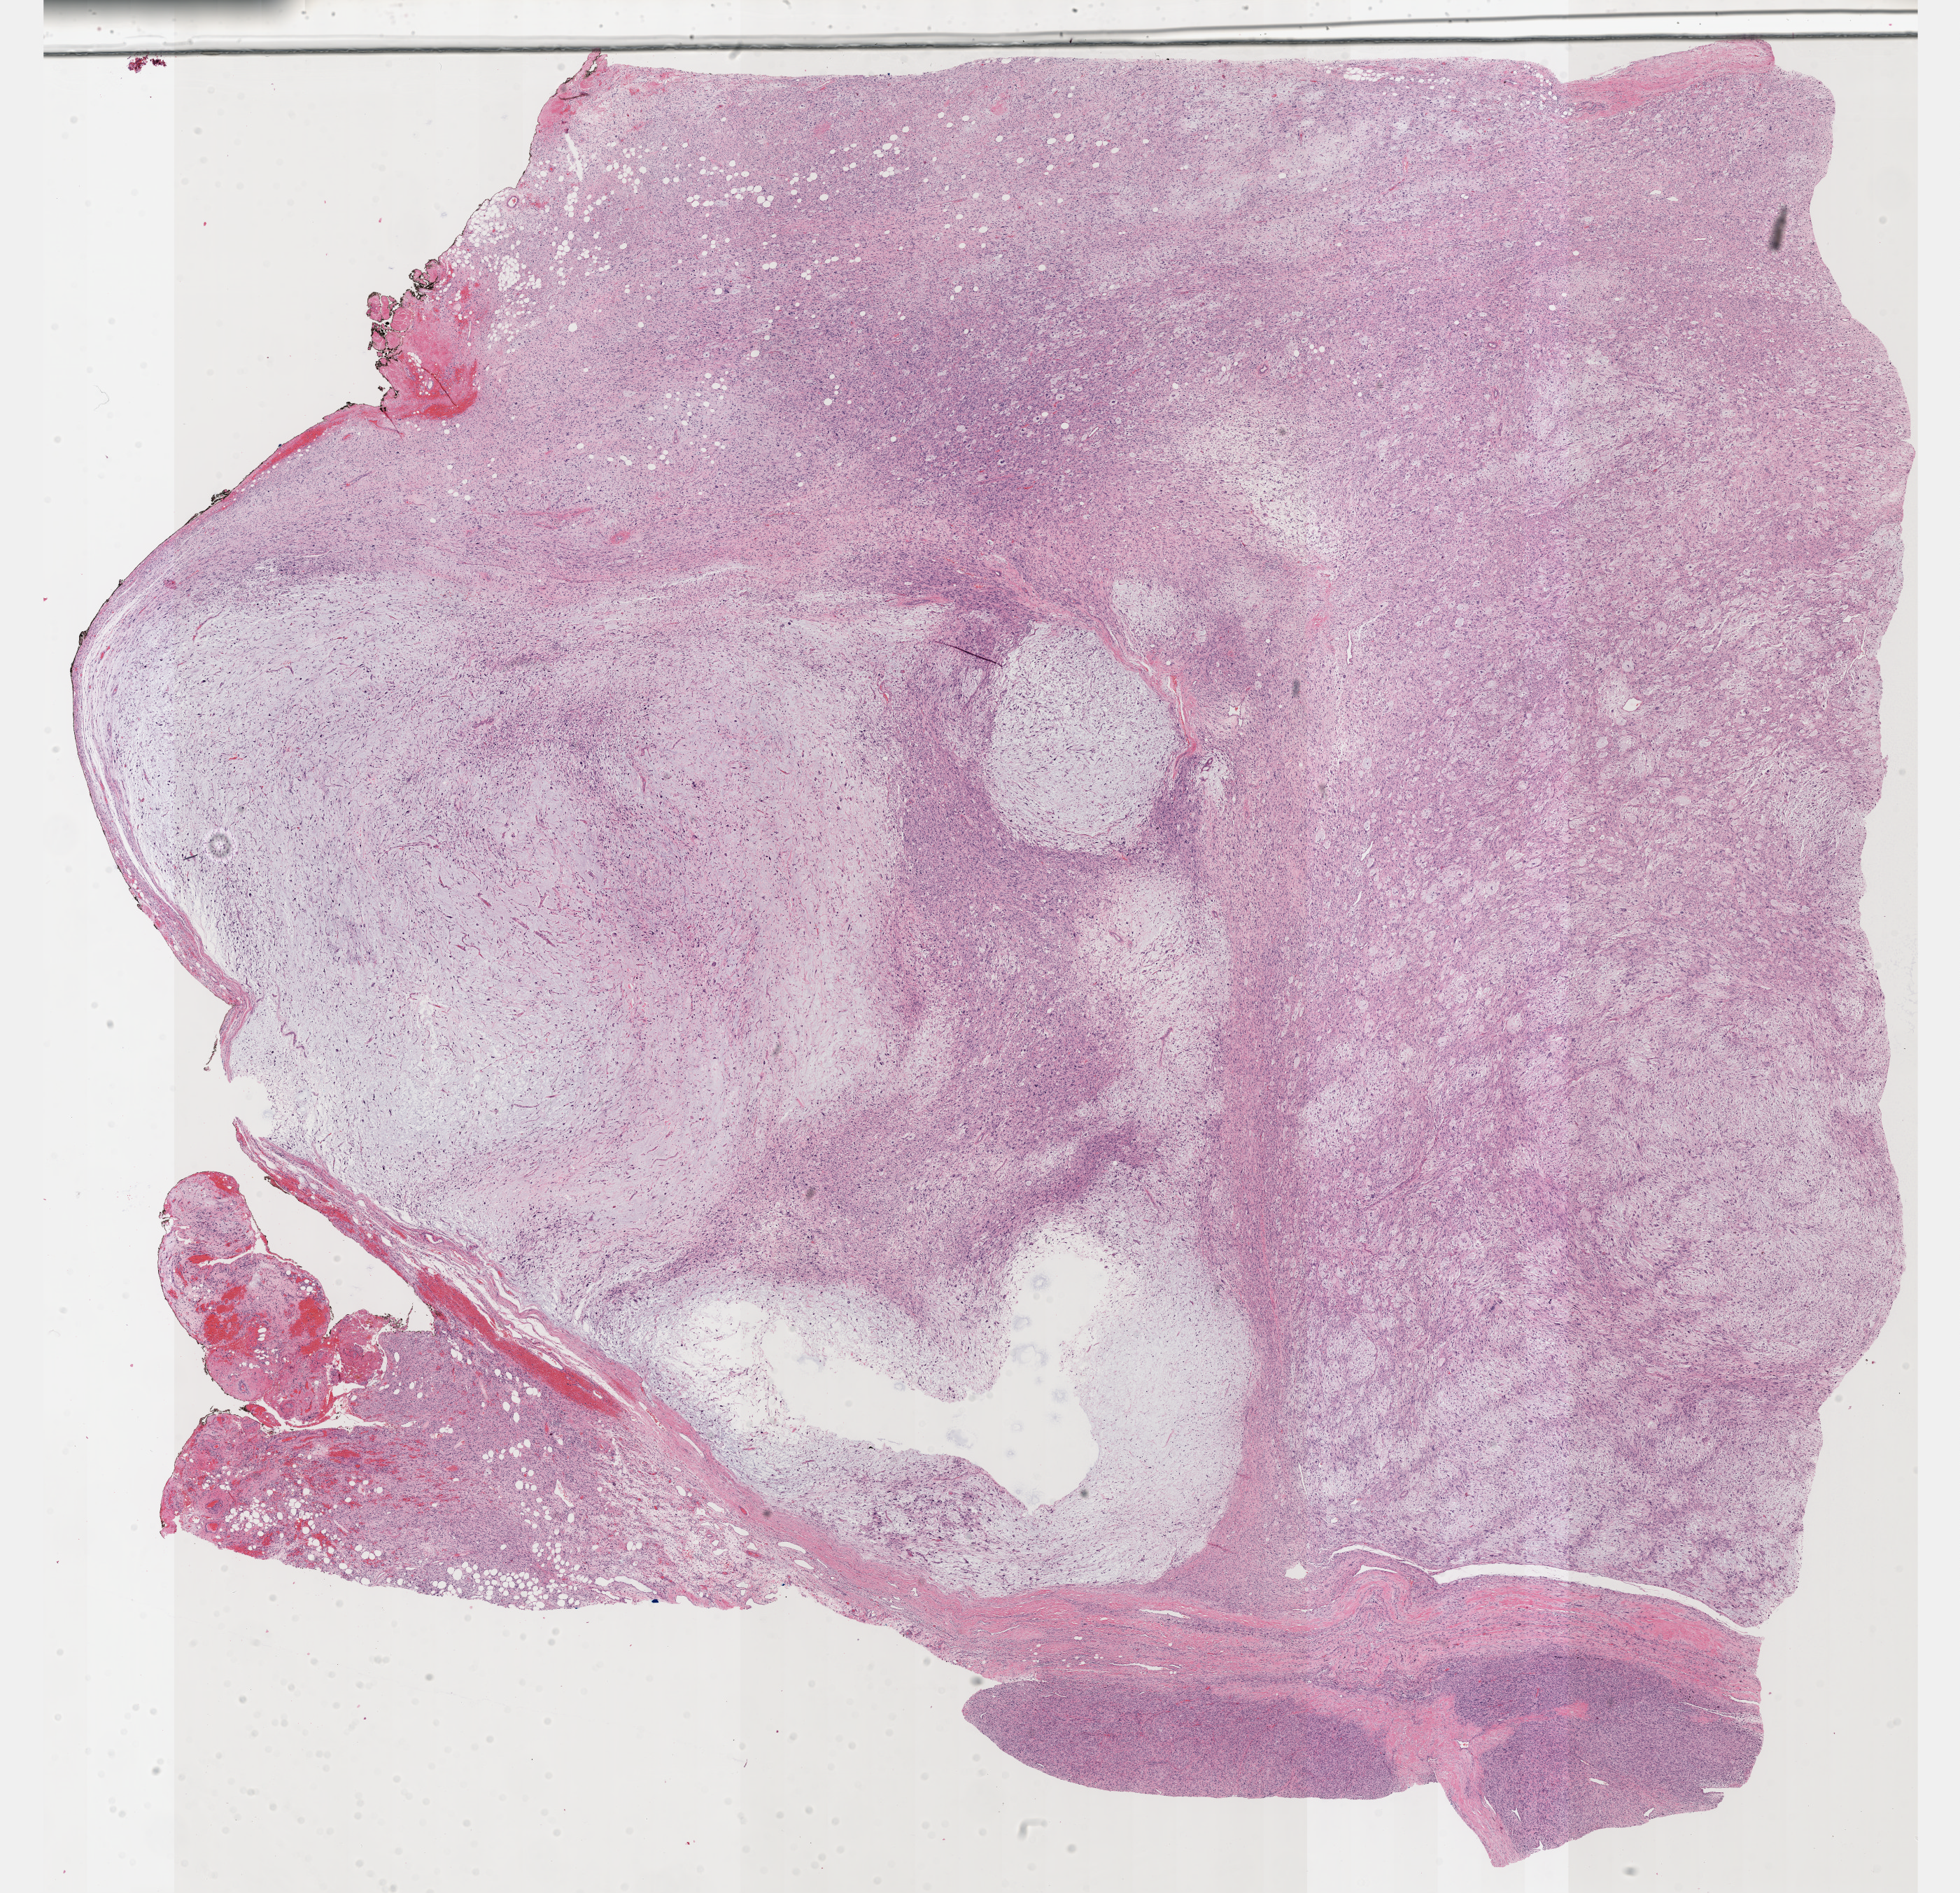
H&E whole-slide image — low-resolution overview of the scanned area, about 22.6 x 21.9 mm; formalin-fixed paraffin-embedded (FFPE) diagnostic section; connective, subcutaneous and other soft tissues, primary tumour sample. Male, age 55 years at initial diagnosis.
Histologic diagnosis: Fibromyxosarcoma (connective, subcutaneous and other soft tissues of lower limb and hip).